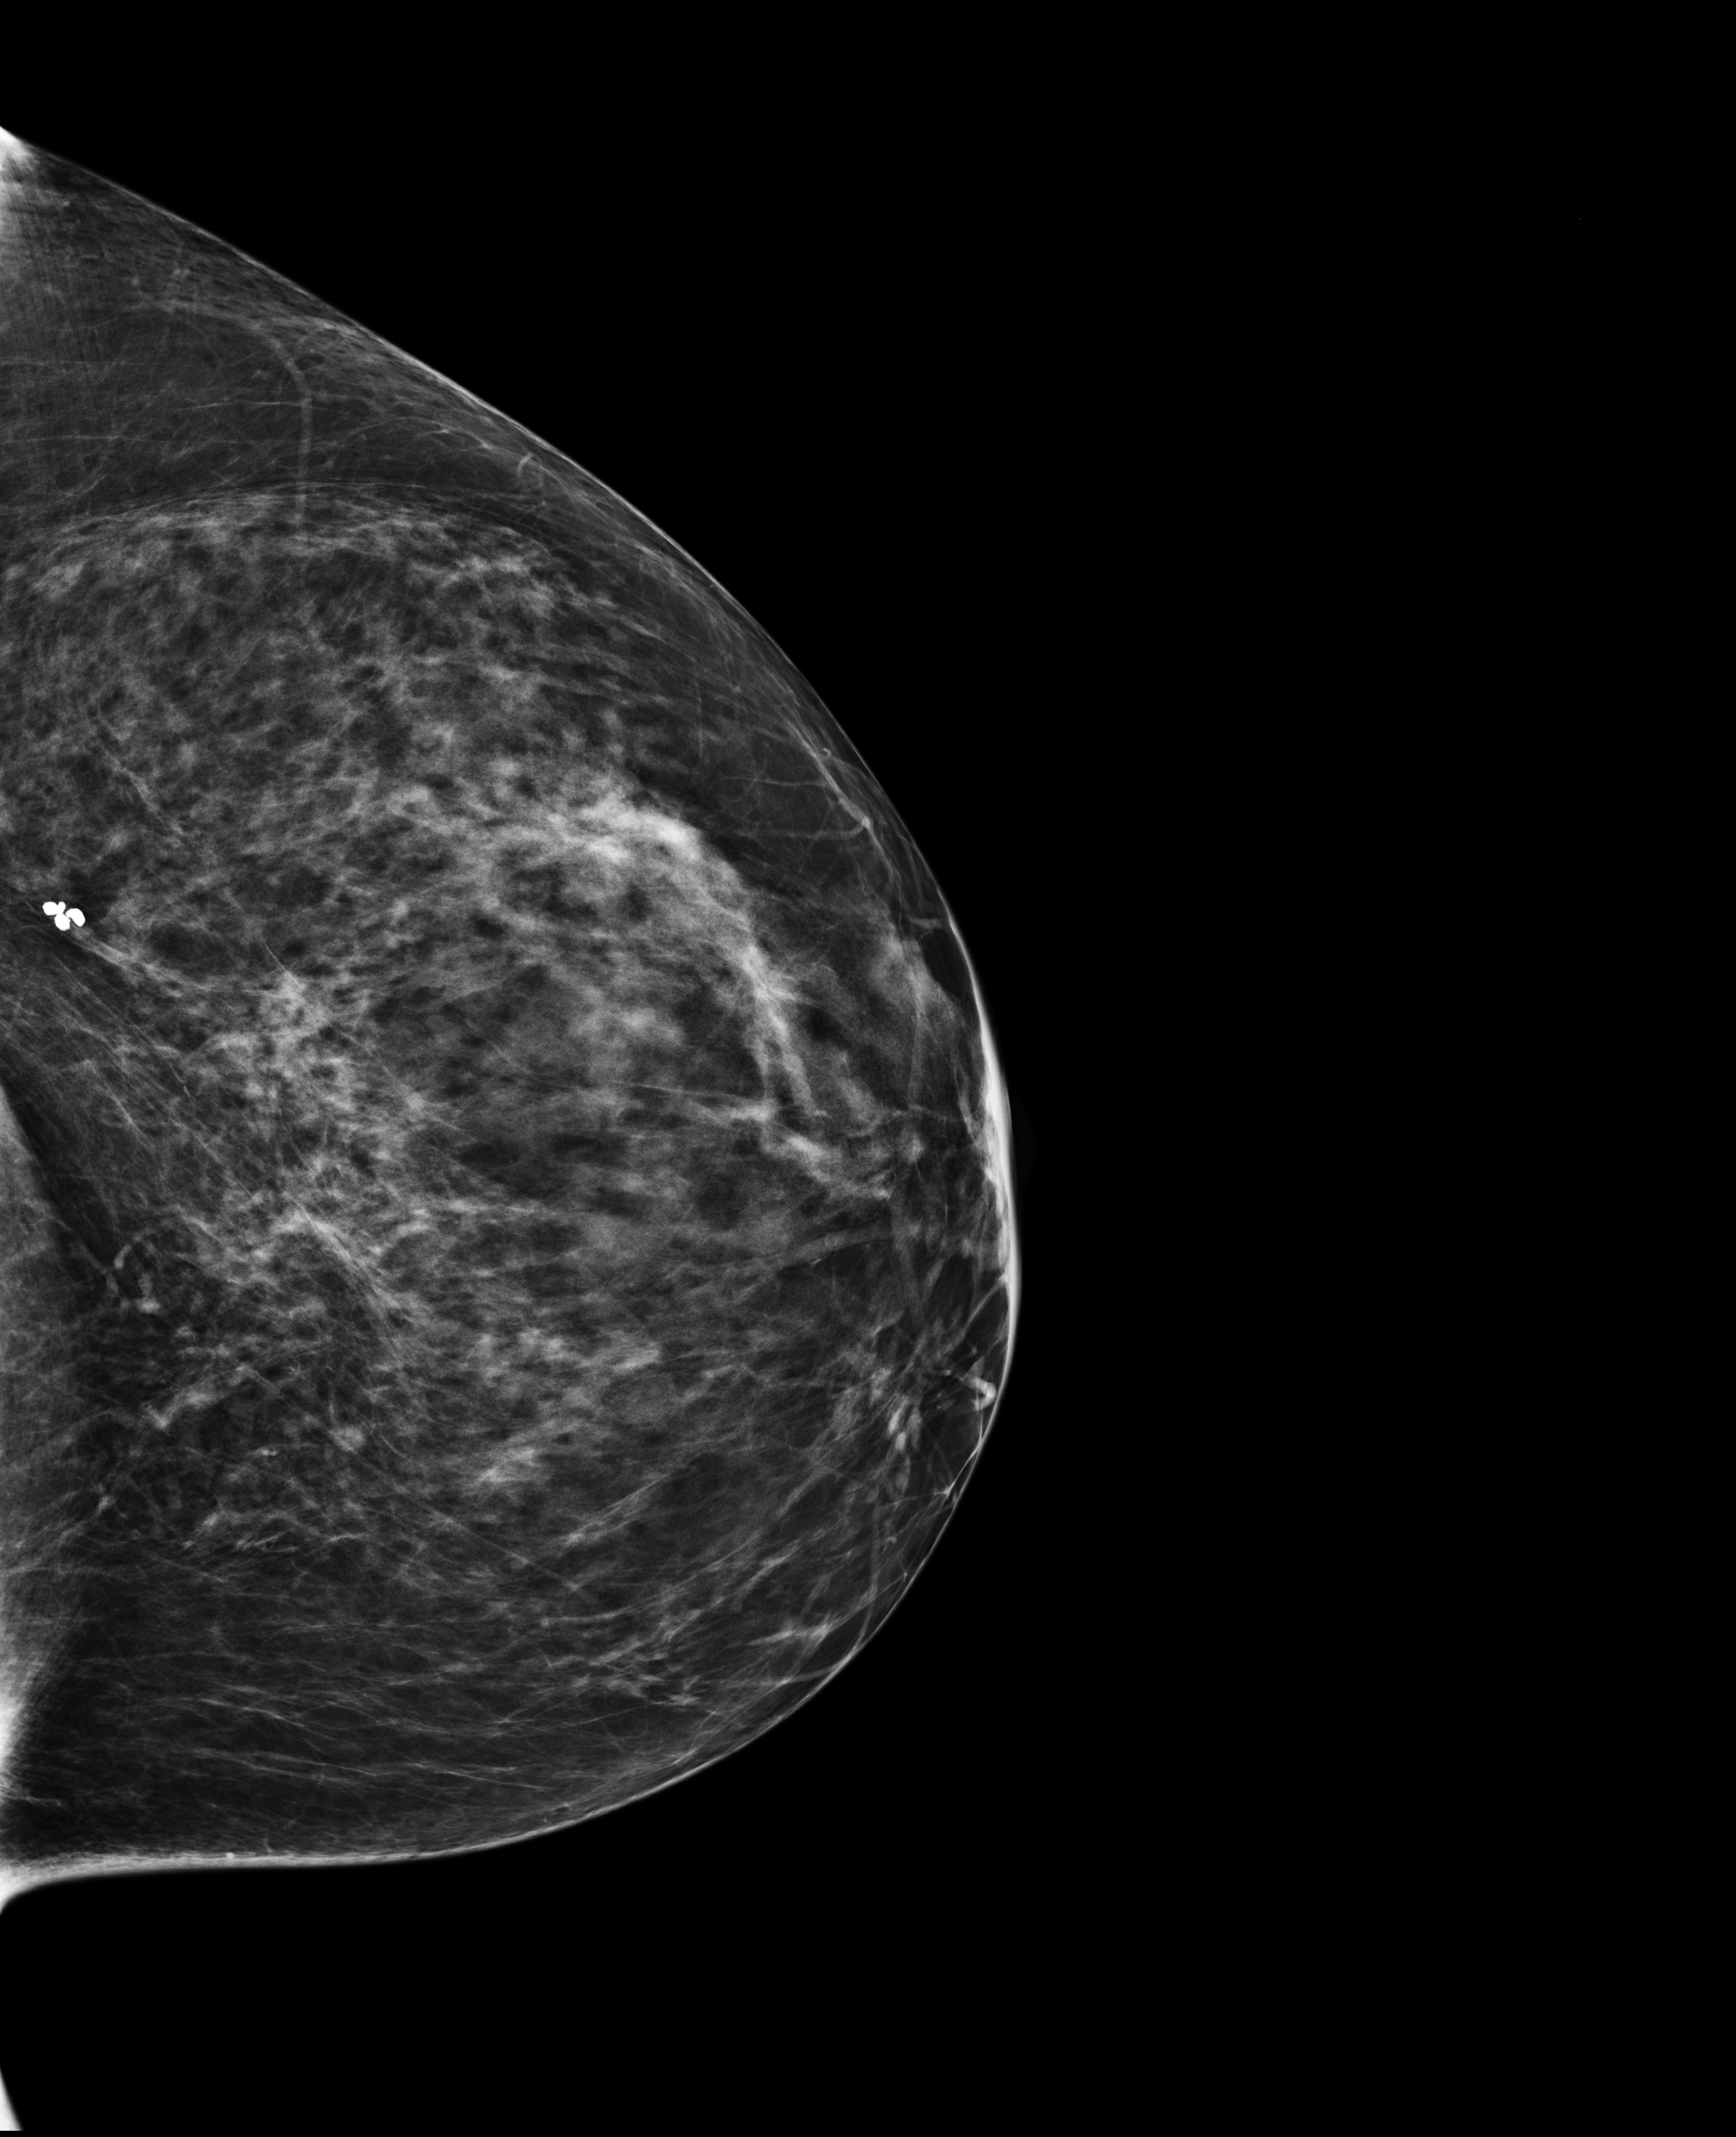
Screening examination, compressed breast thickness 72 mm, system: Selenia Dimensions.
Image type: full-field digital mammogram. Breast: left. Projection: CC view.